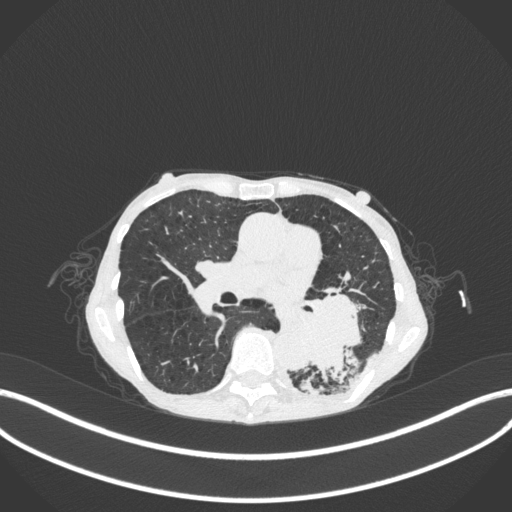
Chest CT, one axial slice; position 142 of 347 along the scan axis; reconstruction kernel B31f; 120 kVp; lung window (W 1500 / L -600 HU); 1 mm slice thickness; 512 × 512 image matrix, field of view 400 × 400 mm. Patient: female, 70 years. From the clinical record (not read from this slice): clinical TNM (as recorded): T3 N0 M0.
Structures marked on this image (rectangle marked by the reading radiologist):
- lung tumour (recorded histology: small cell carcinoma): box from (x=297, y=287) to (x=369, y=385) px